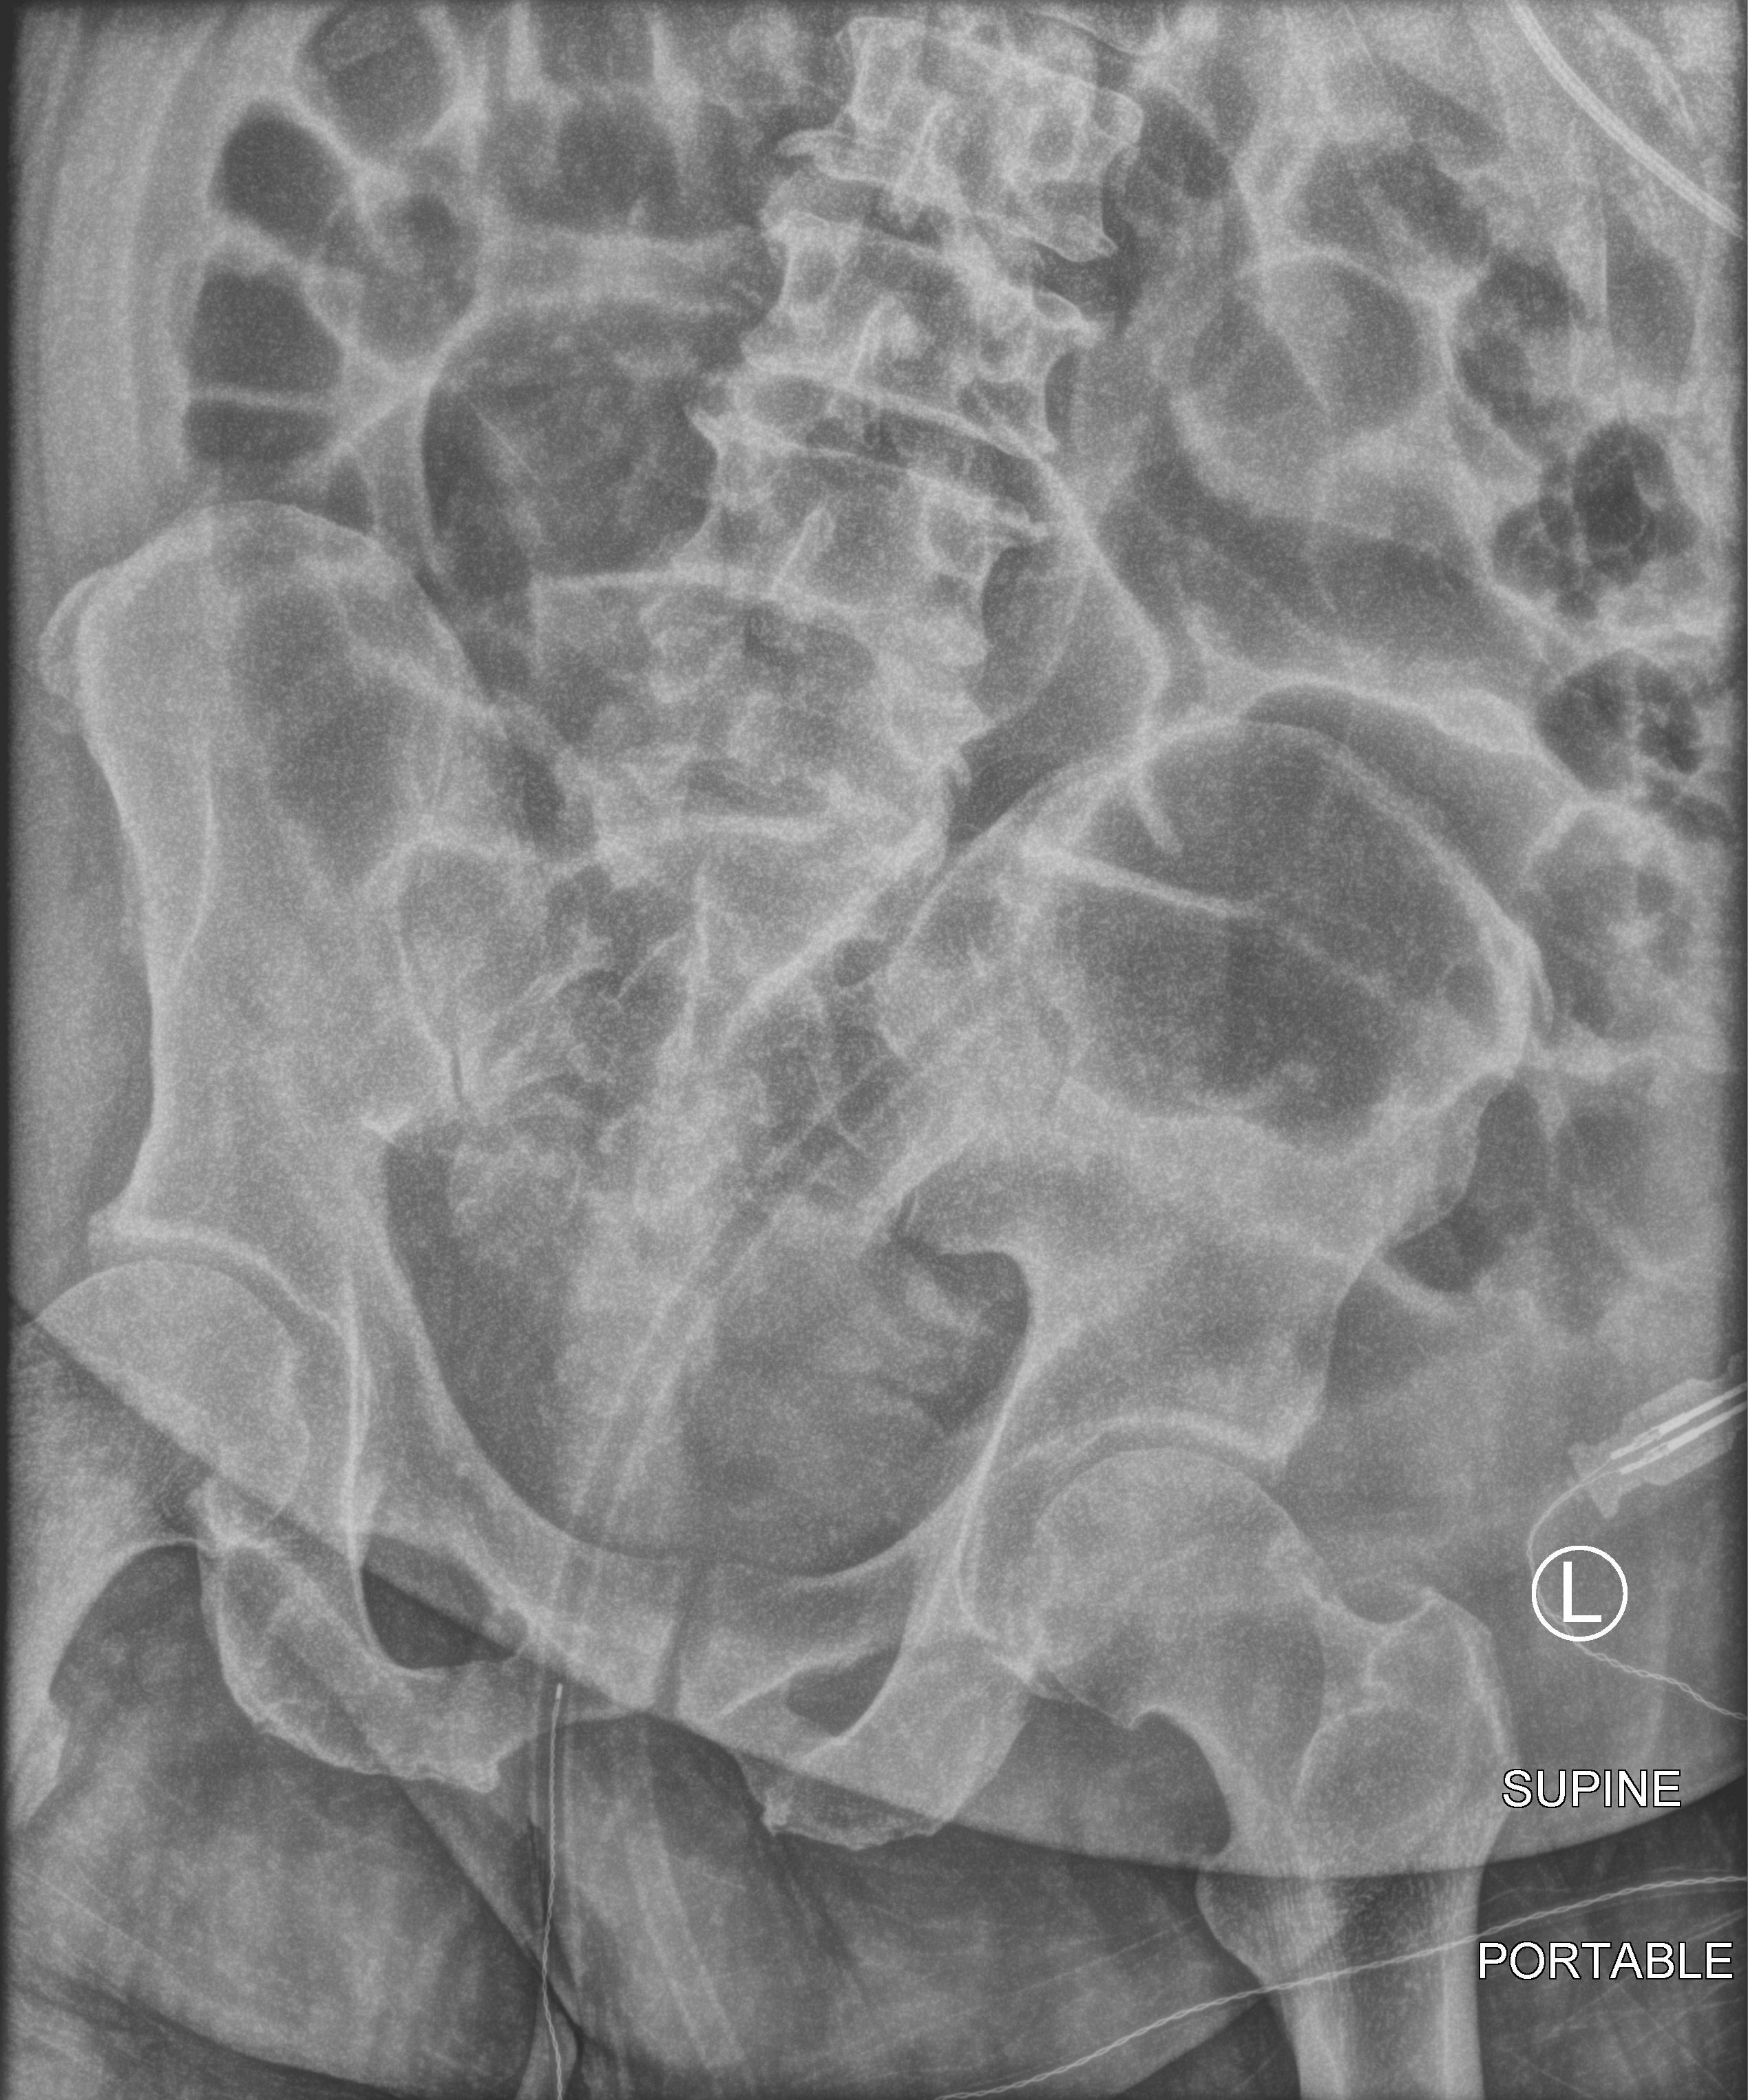
Portable abdomen radiograph; anteroposterior (AP) projection. Male patient hospitalised with COVID-19, age 18–59 years.
From the hospital-stay record, not from the radiograph (when in the stay this image was taken is not recorded): admitted to intensive care during this hospital stay: yes; mechanically ventilated during this hospital stay: yes.